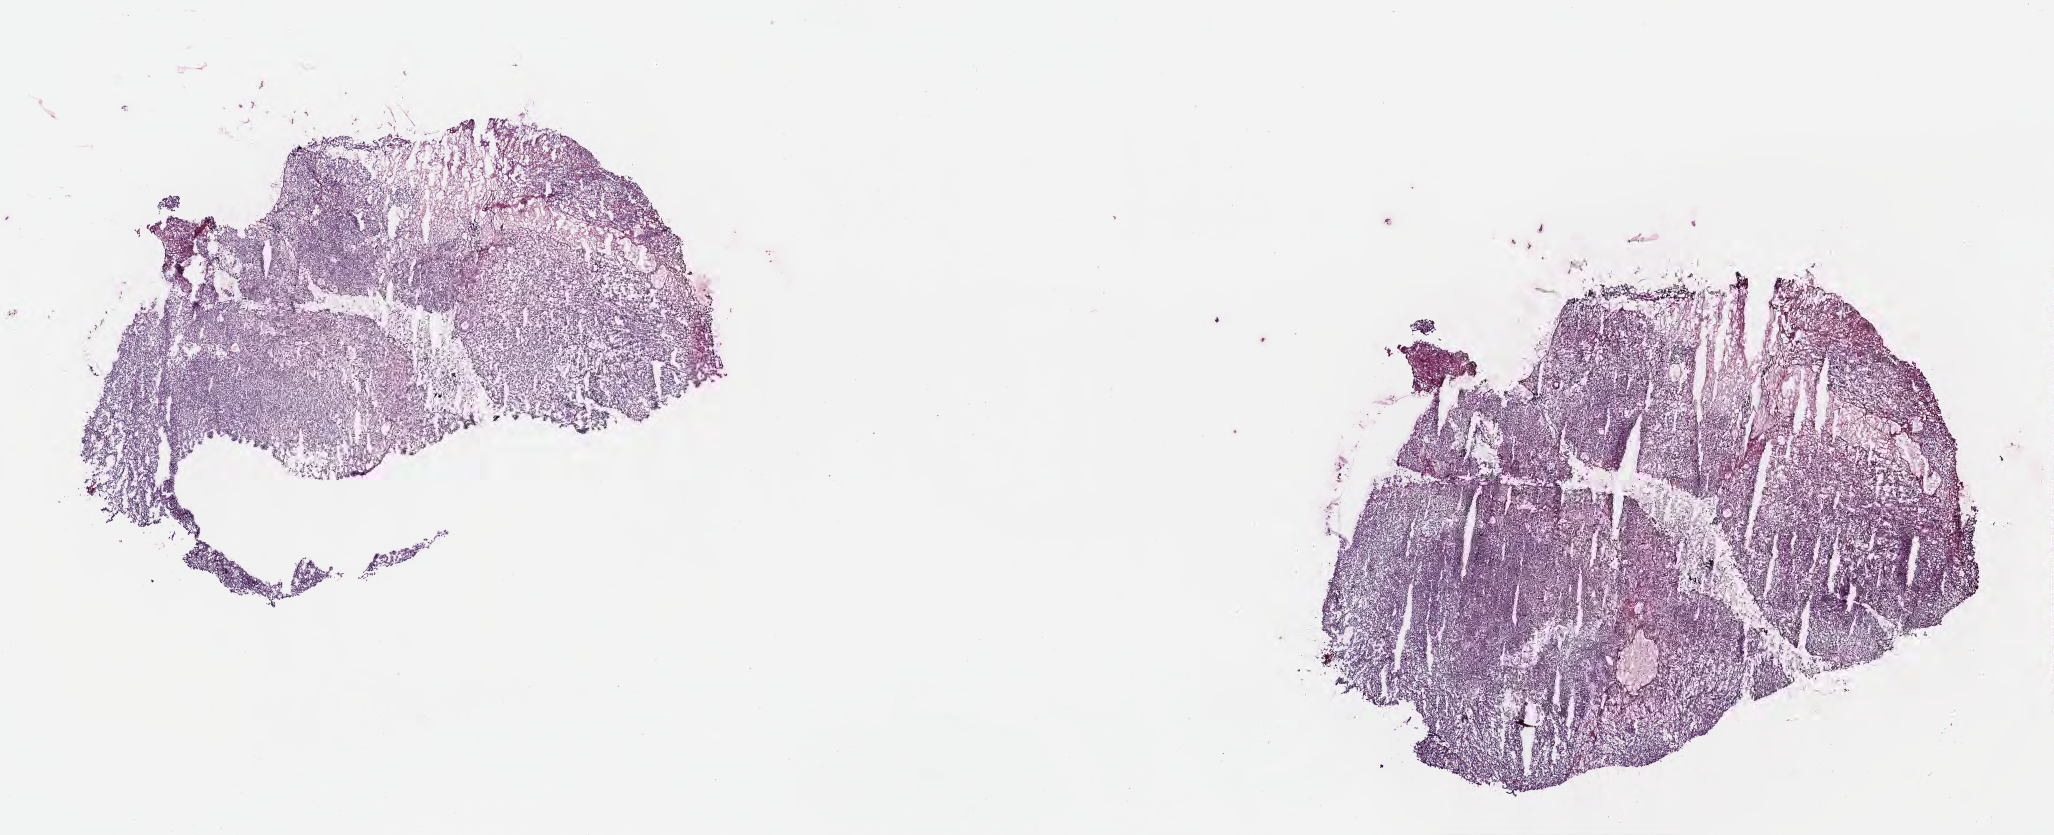
Digitized haematoxylin and eosin-stained section — shown as a low-resolution overview of the whole scanned area (about 16.6 x 6.7 mm). Frozen section (tissue freezing medium). Specimen: primary tumor. Site: cranium. Female, age 5 years at initial diagnosis. Slide review estimates, as recorded: tumor cells 80%, tumor nuclei 90%, stromal cells 10%, necrosis 5%, normal cells 5%. Inflammatory infiltration, as recorded: lymphocyte infiltration 80%, monocyte infiltration 10%, neutrophil infiltration 0%.
Histologic diagnosis: Burkitt lymphoma, NOS. Ann Arbor stage (patient): Stage I.